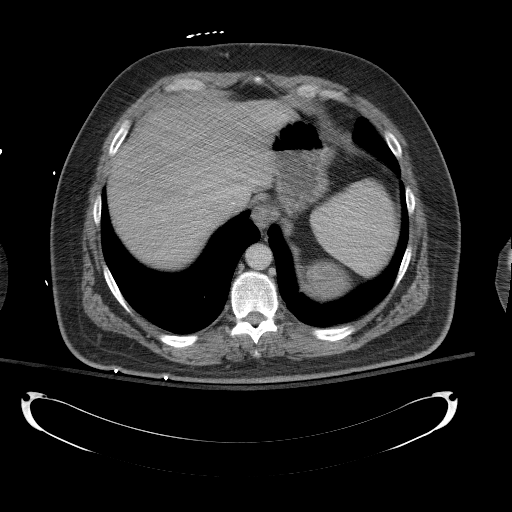
Contrast-enhanced abdominal CT, one axial slice; position 100 of 154 along the scan axis; intravenous contrast given; soft-tissue window (W 400 / L 40 HU); 5 mm slice thickness; 512 × 512 image matrix, field of view 467 × 467 mm. Patient: male, 43 years. From the clinical record (not read from this slice): diagnosis: adrenocortical carcinoma; tumour side: left adrenal; tumour size at pathology: 9.8 cm; Ki-67 index: 30 %; stage (as recorded): 2.
Structures marked on this image (semi-automatic segmentation, software-assisted and operator-edited):
- mass: bounding box <308,263,350,297> (left, top, right, bottom; pixels)